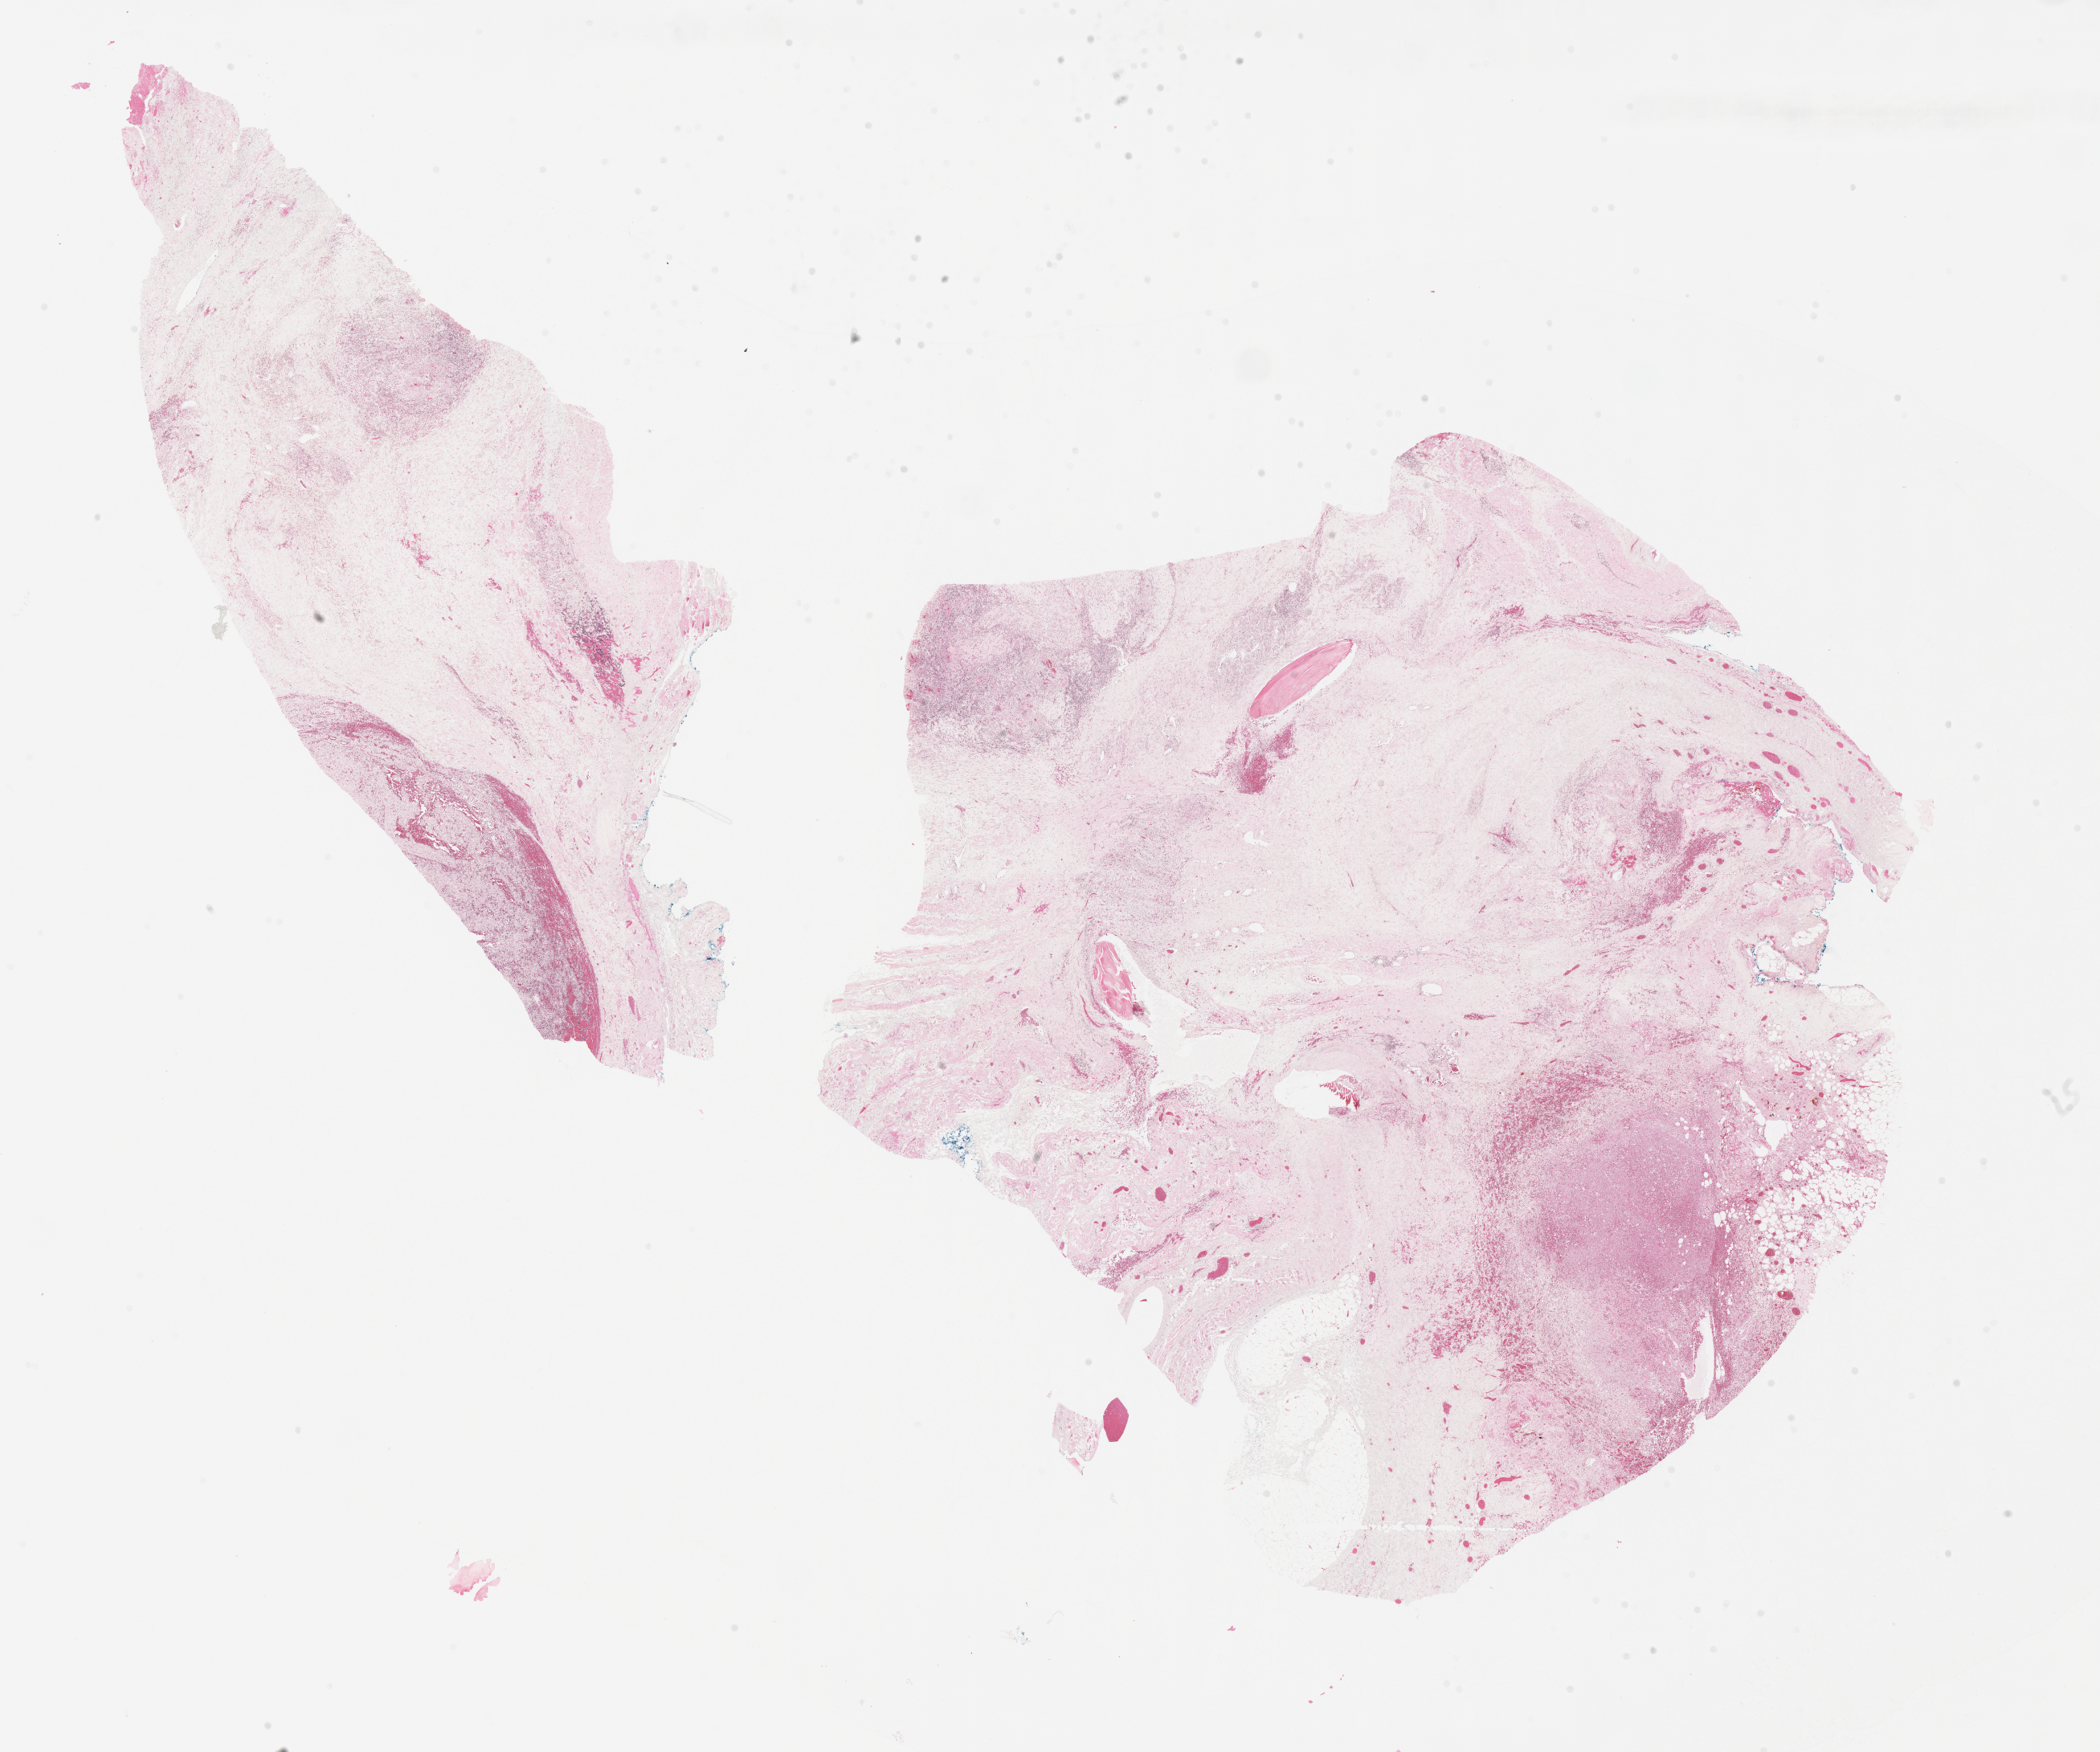
Hematoxylin and eosin (H&E) whole-slide image of tumor tissue — low-resolution overview of the scanned area, about 21.1 x 17.6 mm. Formalin-fixed, paraffin-embedded (FFPE) tissue. Sample anatomic site: temple, right. Patient: female, age 6.9 years at diagnosis.
• stage (as recorded): 1
• primary site (case record): scalp
• diagnosis: rhabdomyosarcoma; histological classification: alveolar rhabdomyosarcoma
• metastatic status at presentation (as recorded): non-metastatic